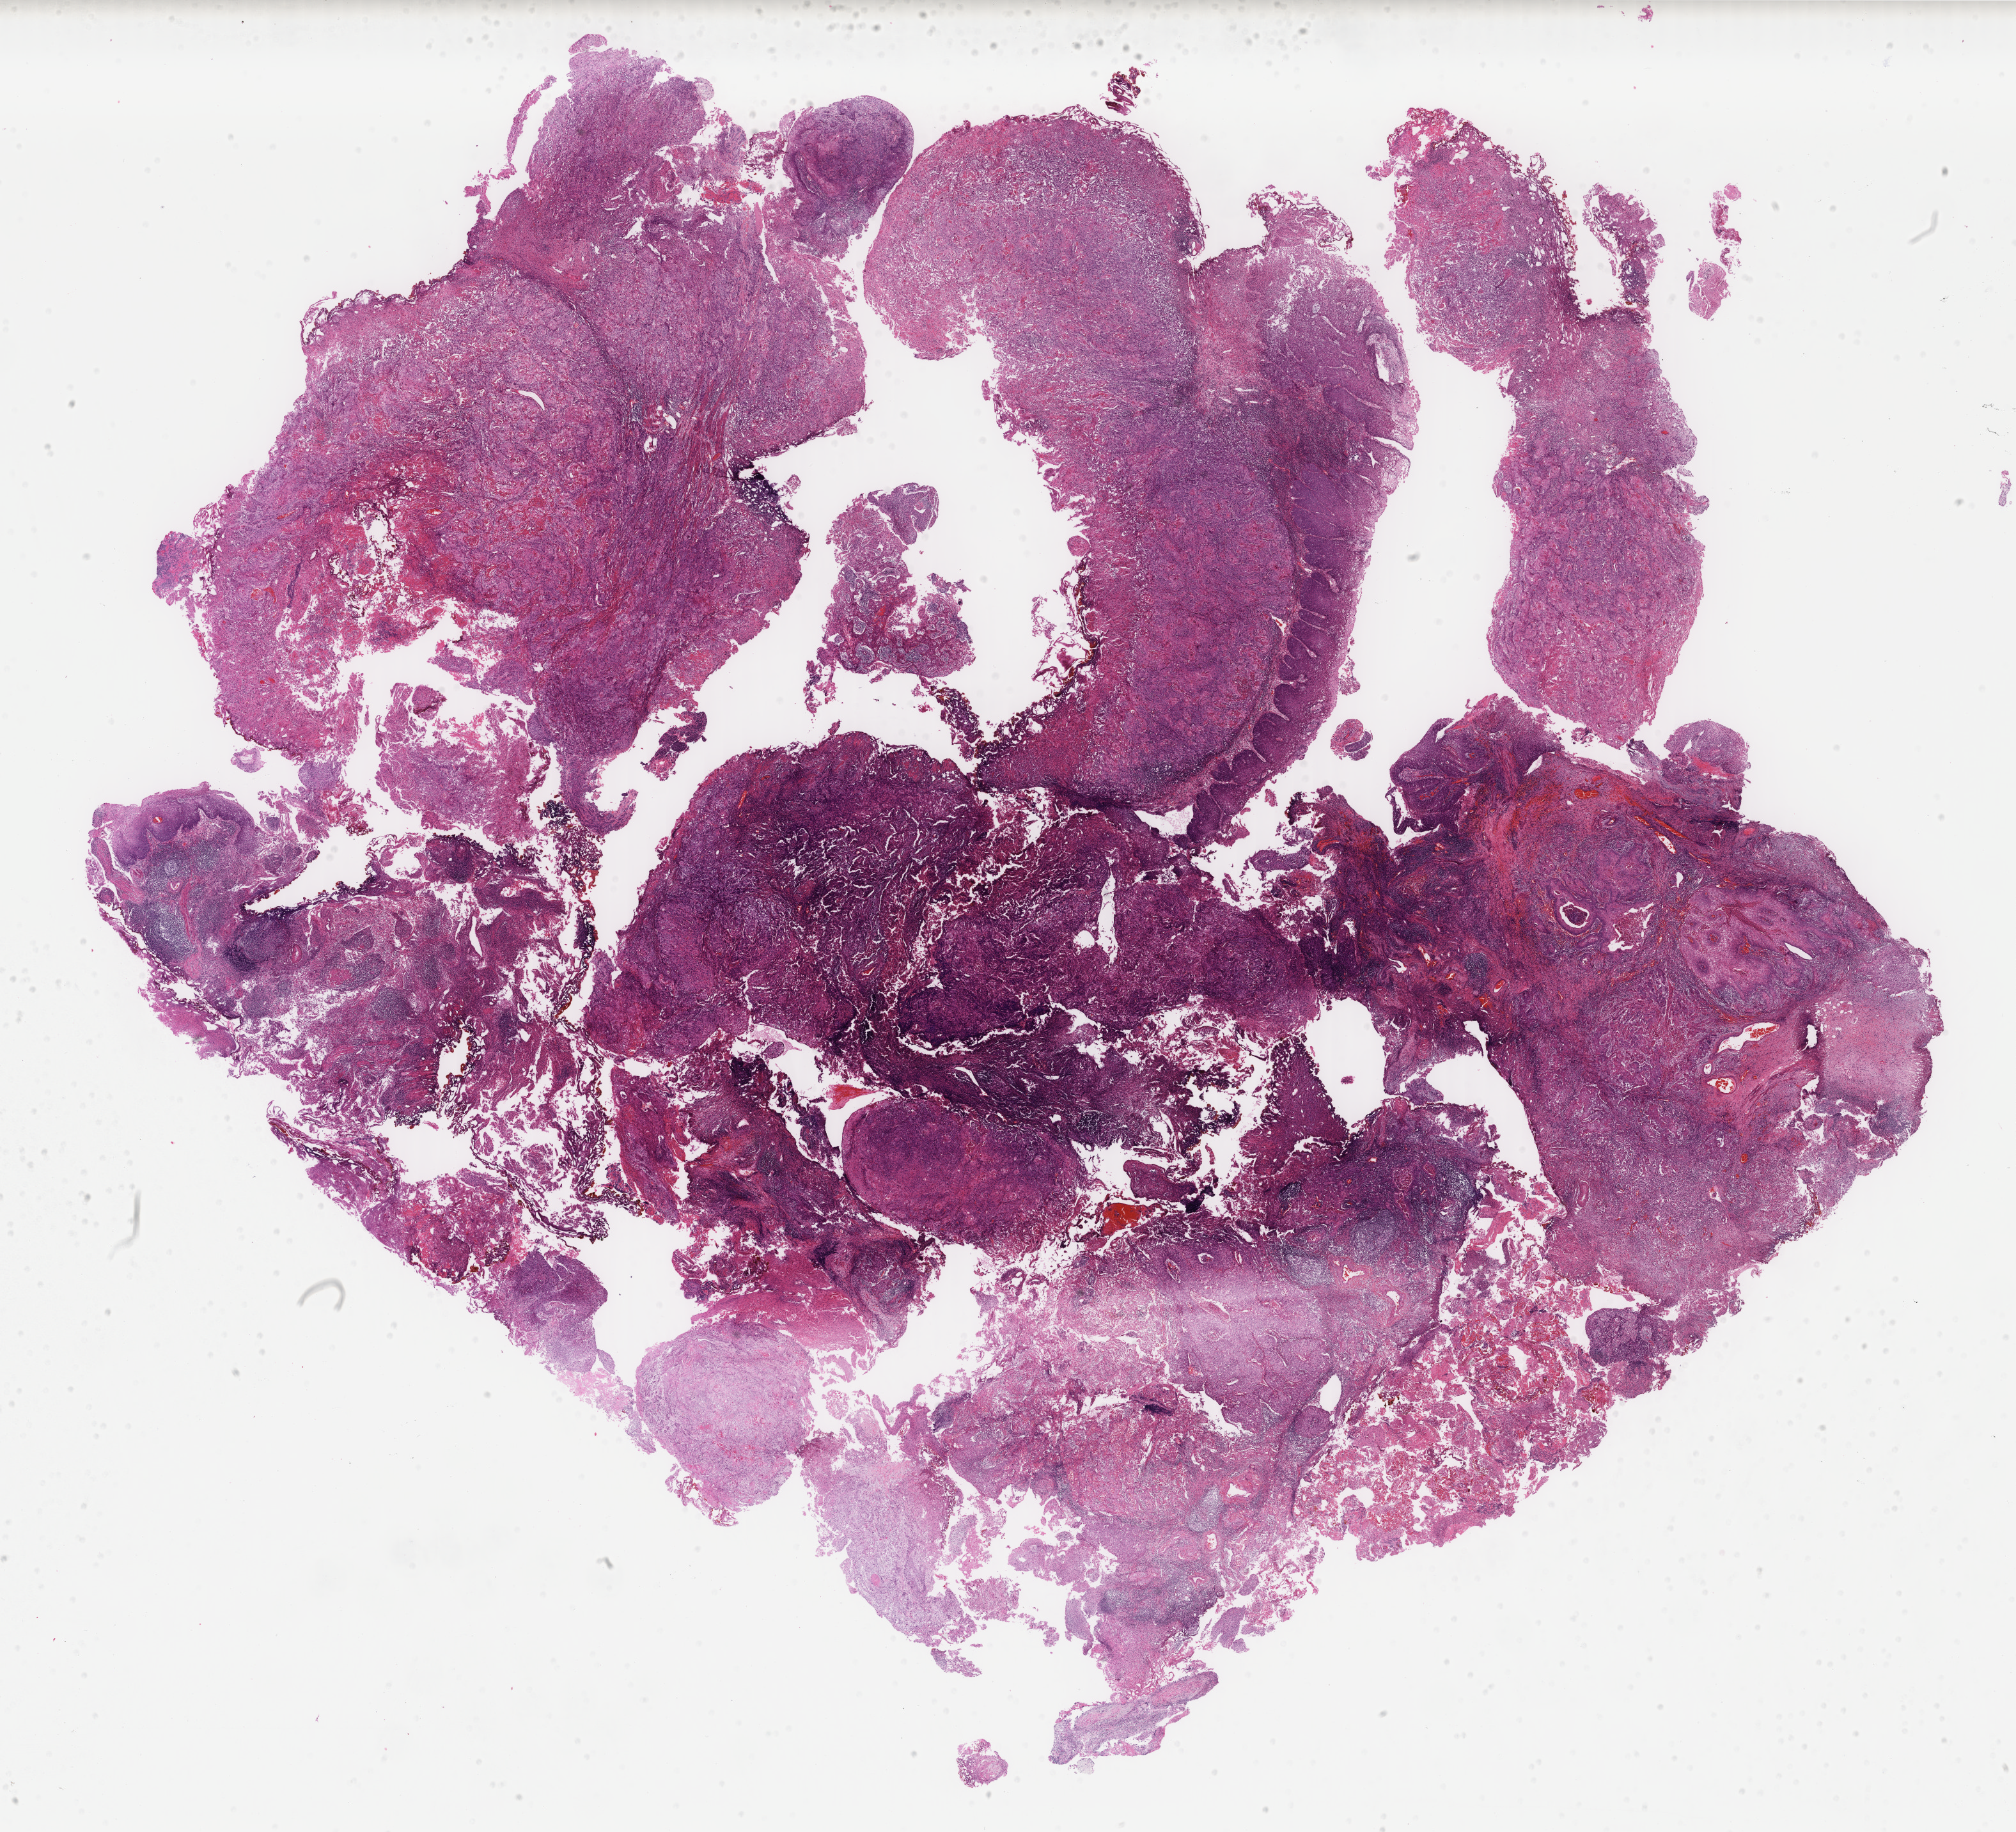
Digitized H&E tissue section (whole slide), whole scanned area (about 25.0 x 22.7 mm, acquisition: 40x scan) shown as a low-resolution overview. Formalin-fixed paraffin-embedded (FFPE) diagnostic section. Sample: primary tumour, bladder. Female, age 56 years at initial diagnosis.
Pathologic diagnosis: Transitional cell carcinoma.